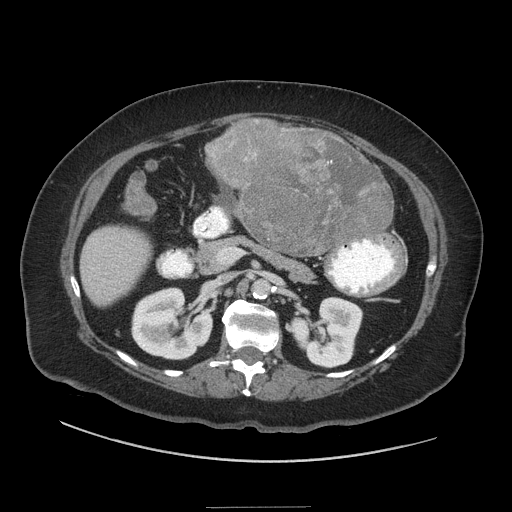
Contrast-enhanced abdominal CT (liver protocol), one axial slice; slice 9 of 81 in the series (ordered by position); 140 kVp; soft-tissue window (W 400 / L 40 HU); 512 × 512 image matrix. Case-level facts recorded for this patient, not image findings: diagnosis: hepatocellular carcinoma (patient treated with transarterial chemoembolisation; whether this scan precedes or follows treatment is not stated here); TNM stage (as recorded): Stage-II.
Structures marked on this image (semi-automatically segmented with operator editing):
- liver parenchyma outside the tumour (the mass and vessels are separate outlines, so this box may not span the whole liver): bounding box <80,118,394,306> (left, top, right, bottom; pixels)
- mass: <206,119,393,256>